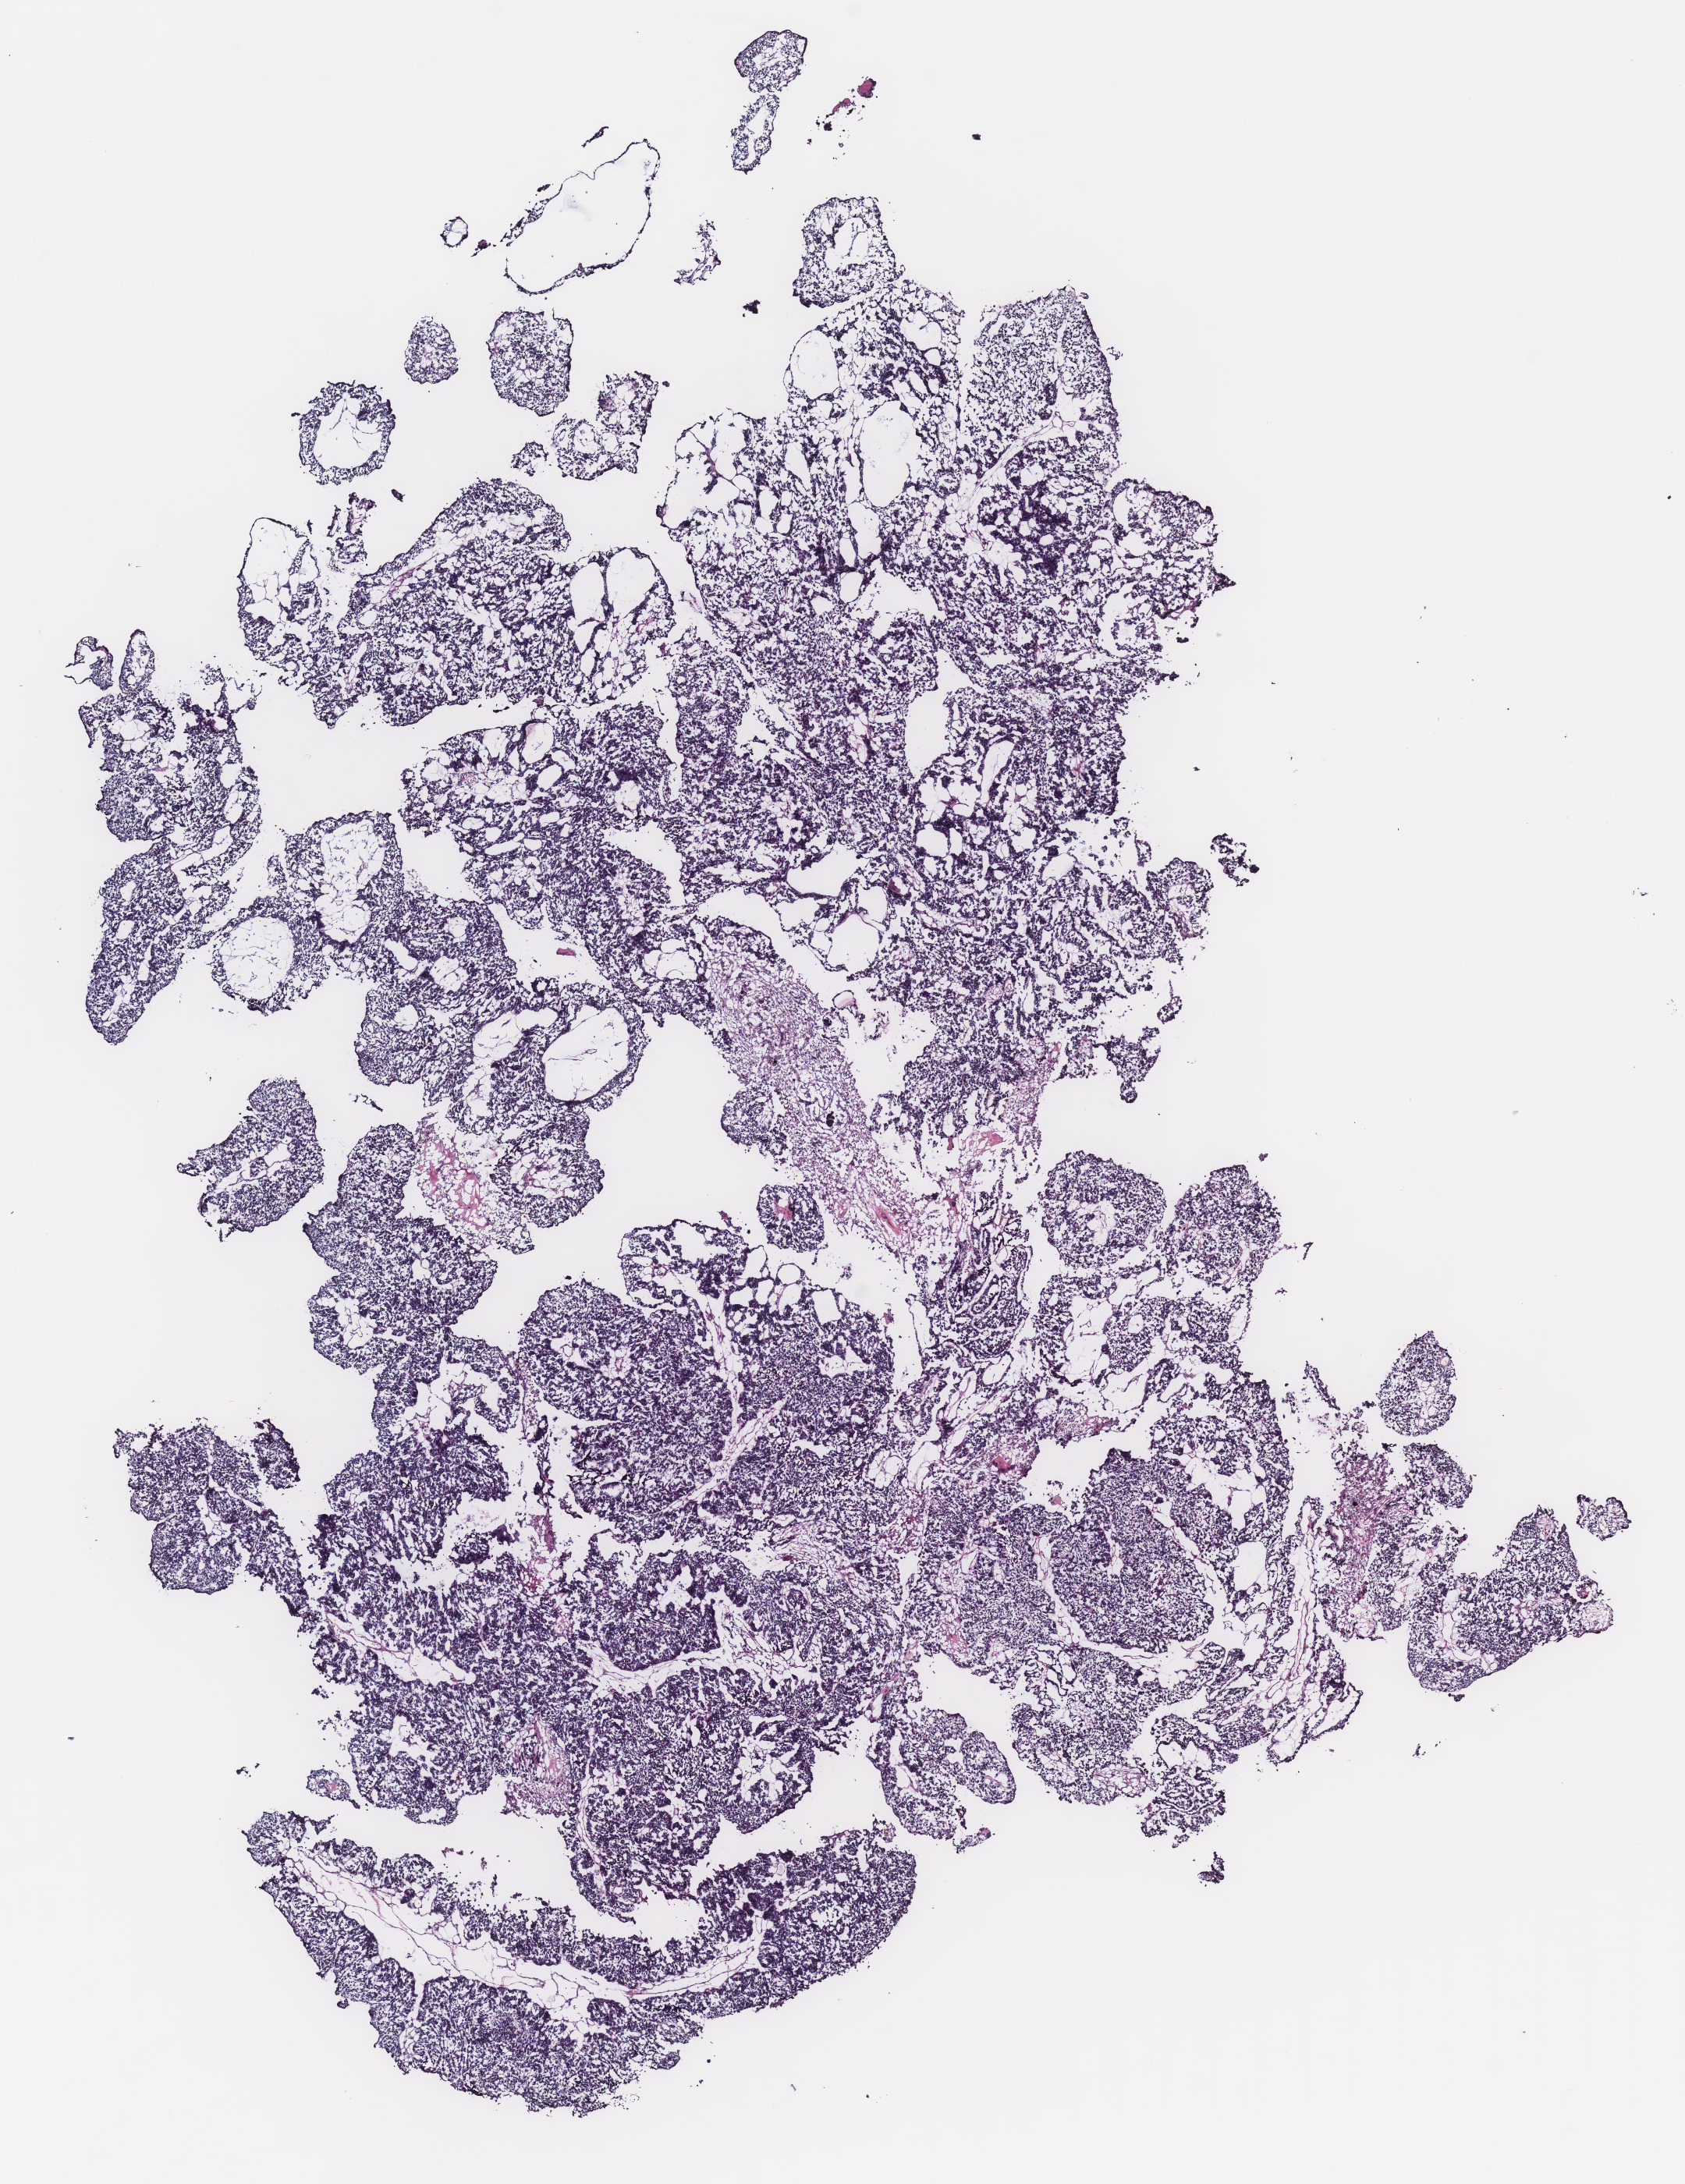
Digitized Hematoxylin and eosin (H&E) stained tissue section (whole slide), a low-resolution overview of the entire scanned area, about 8.6 x 11.2 mm (acquisition: 40x scan). Ovary, tissue type not recorded.
Patient diagnosis (cohort enrolment): ovarian cancer (ovary).